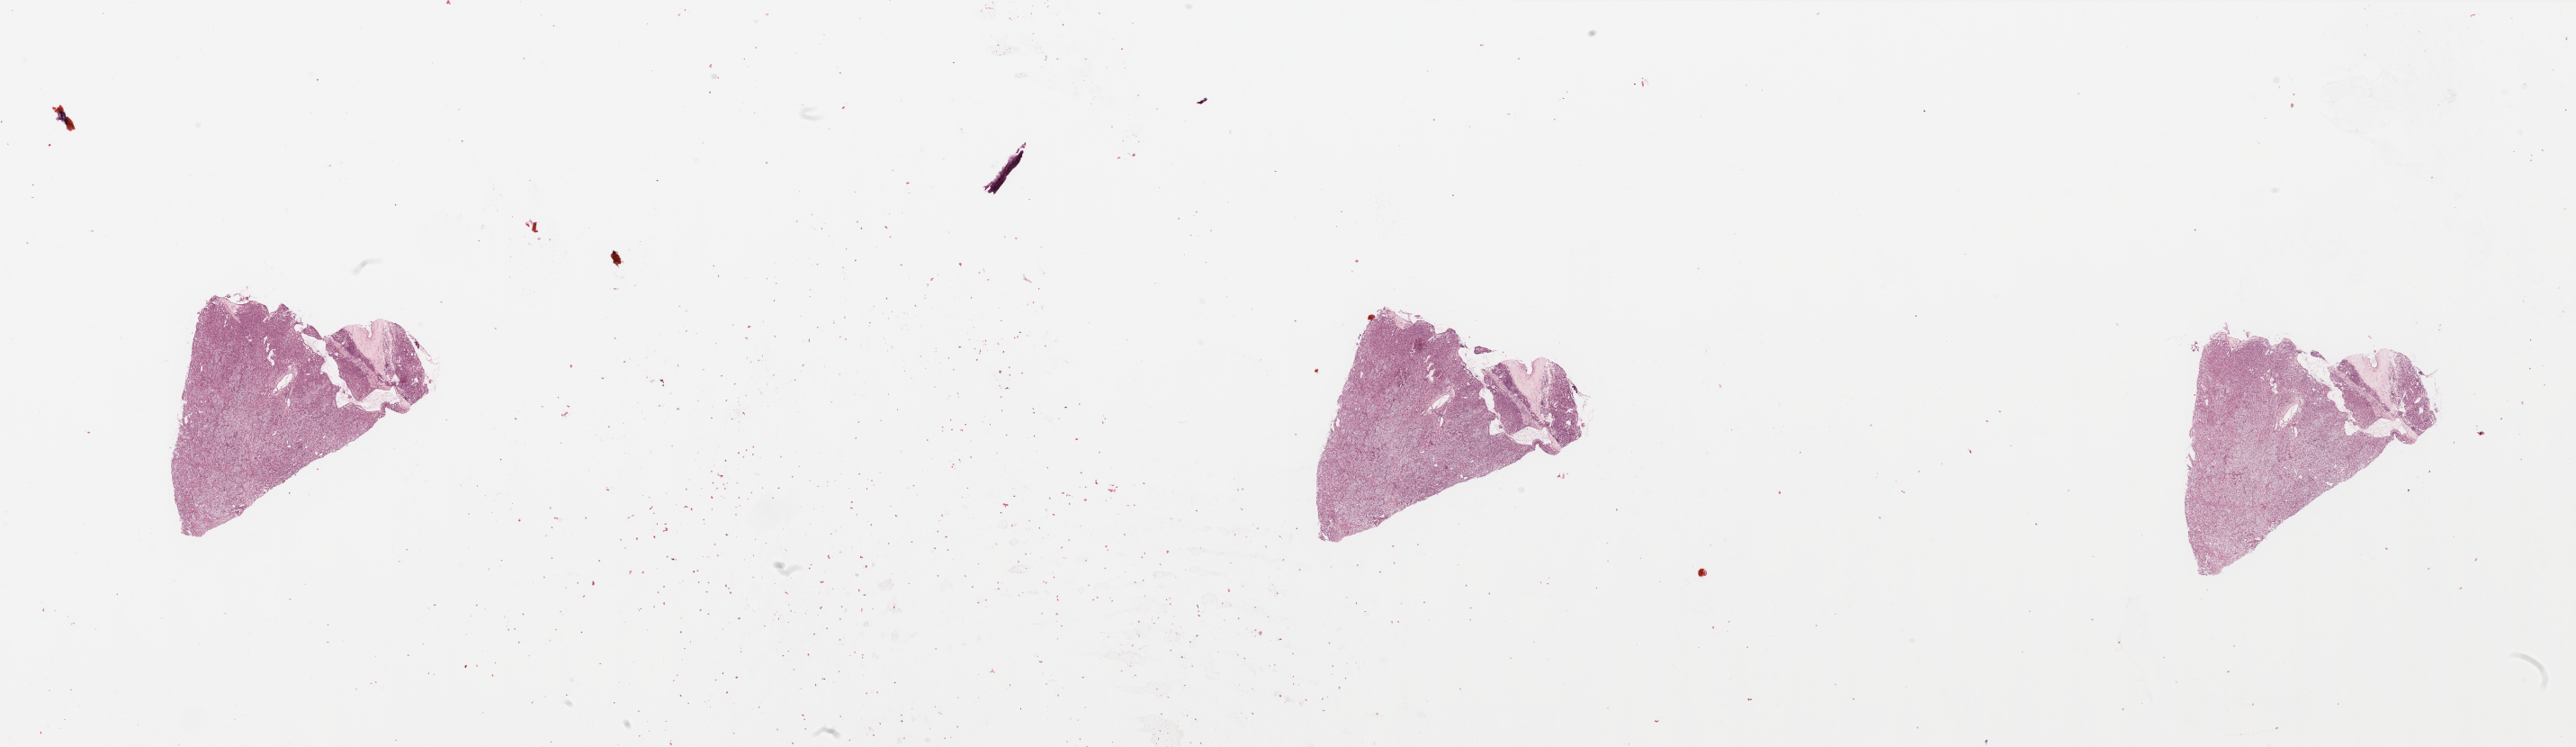
Digitized H&E tissue section (whole slide), a low-resolution overview of the entire scanned area, about 45.3 x 13.1 mm (acquisition: 20x scan); tumour tissue sample, sampled site: kidney. 69-year-old female patient. Pathologist review of this section (percent, as recorded): tumour nuclei 85%, necrosis 0%.
Diagnosis: Renal cell carcinoma, NOS.